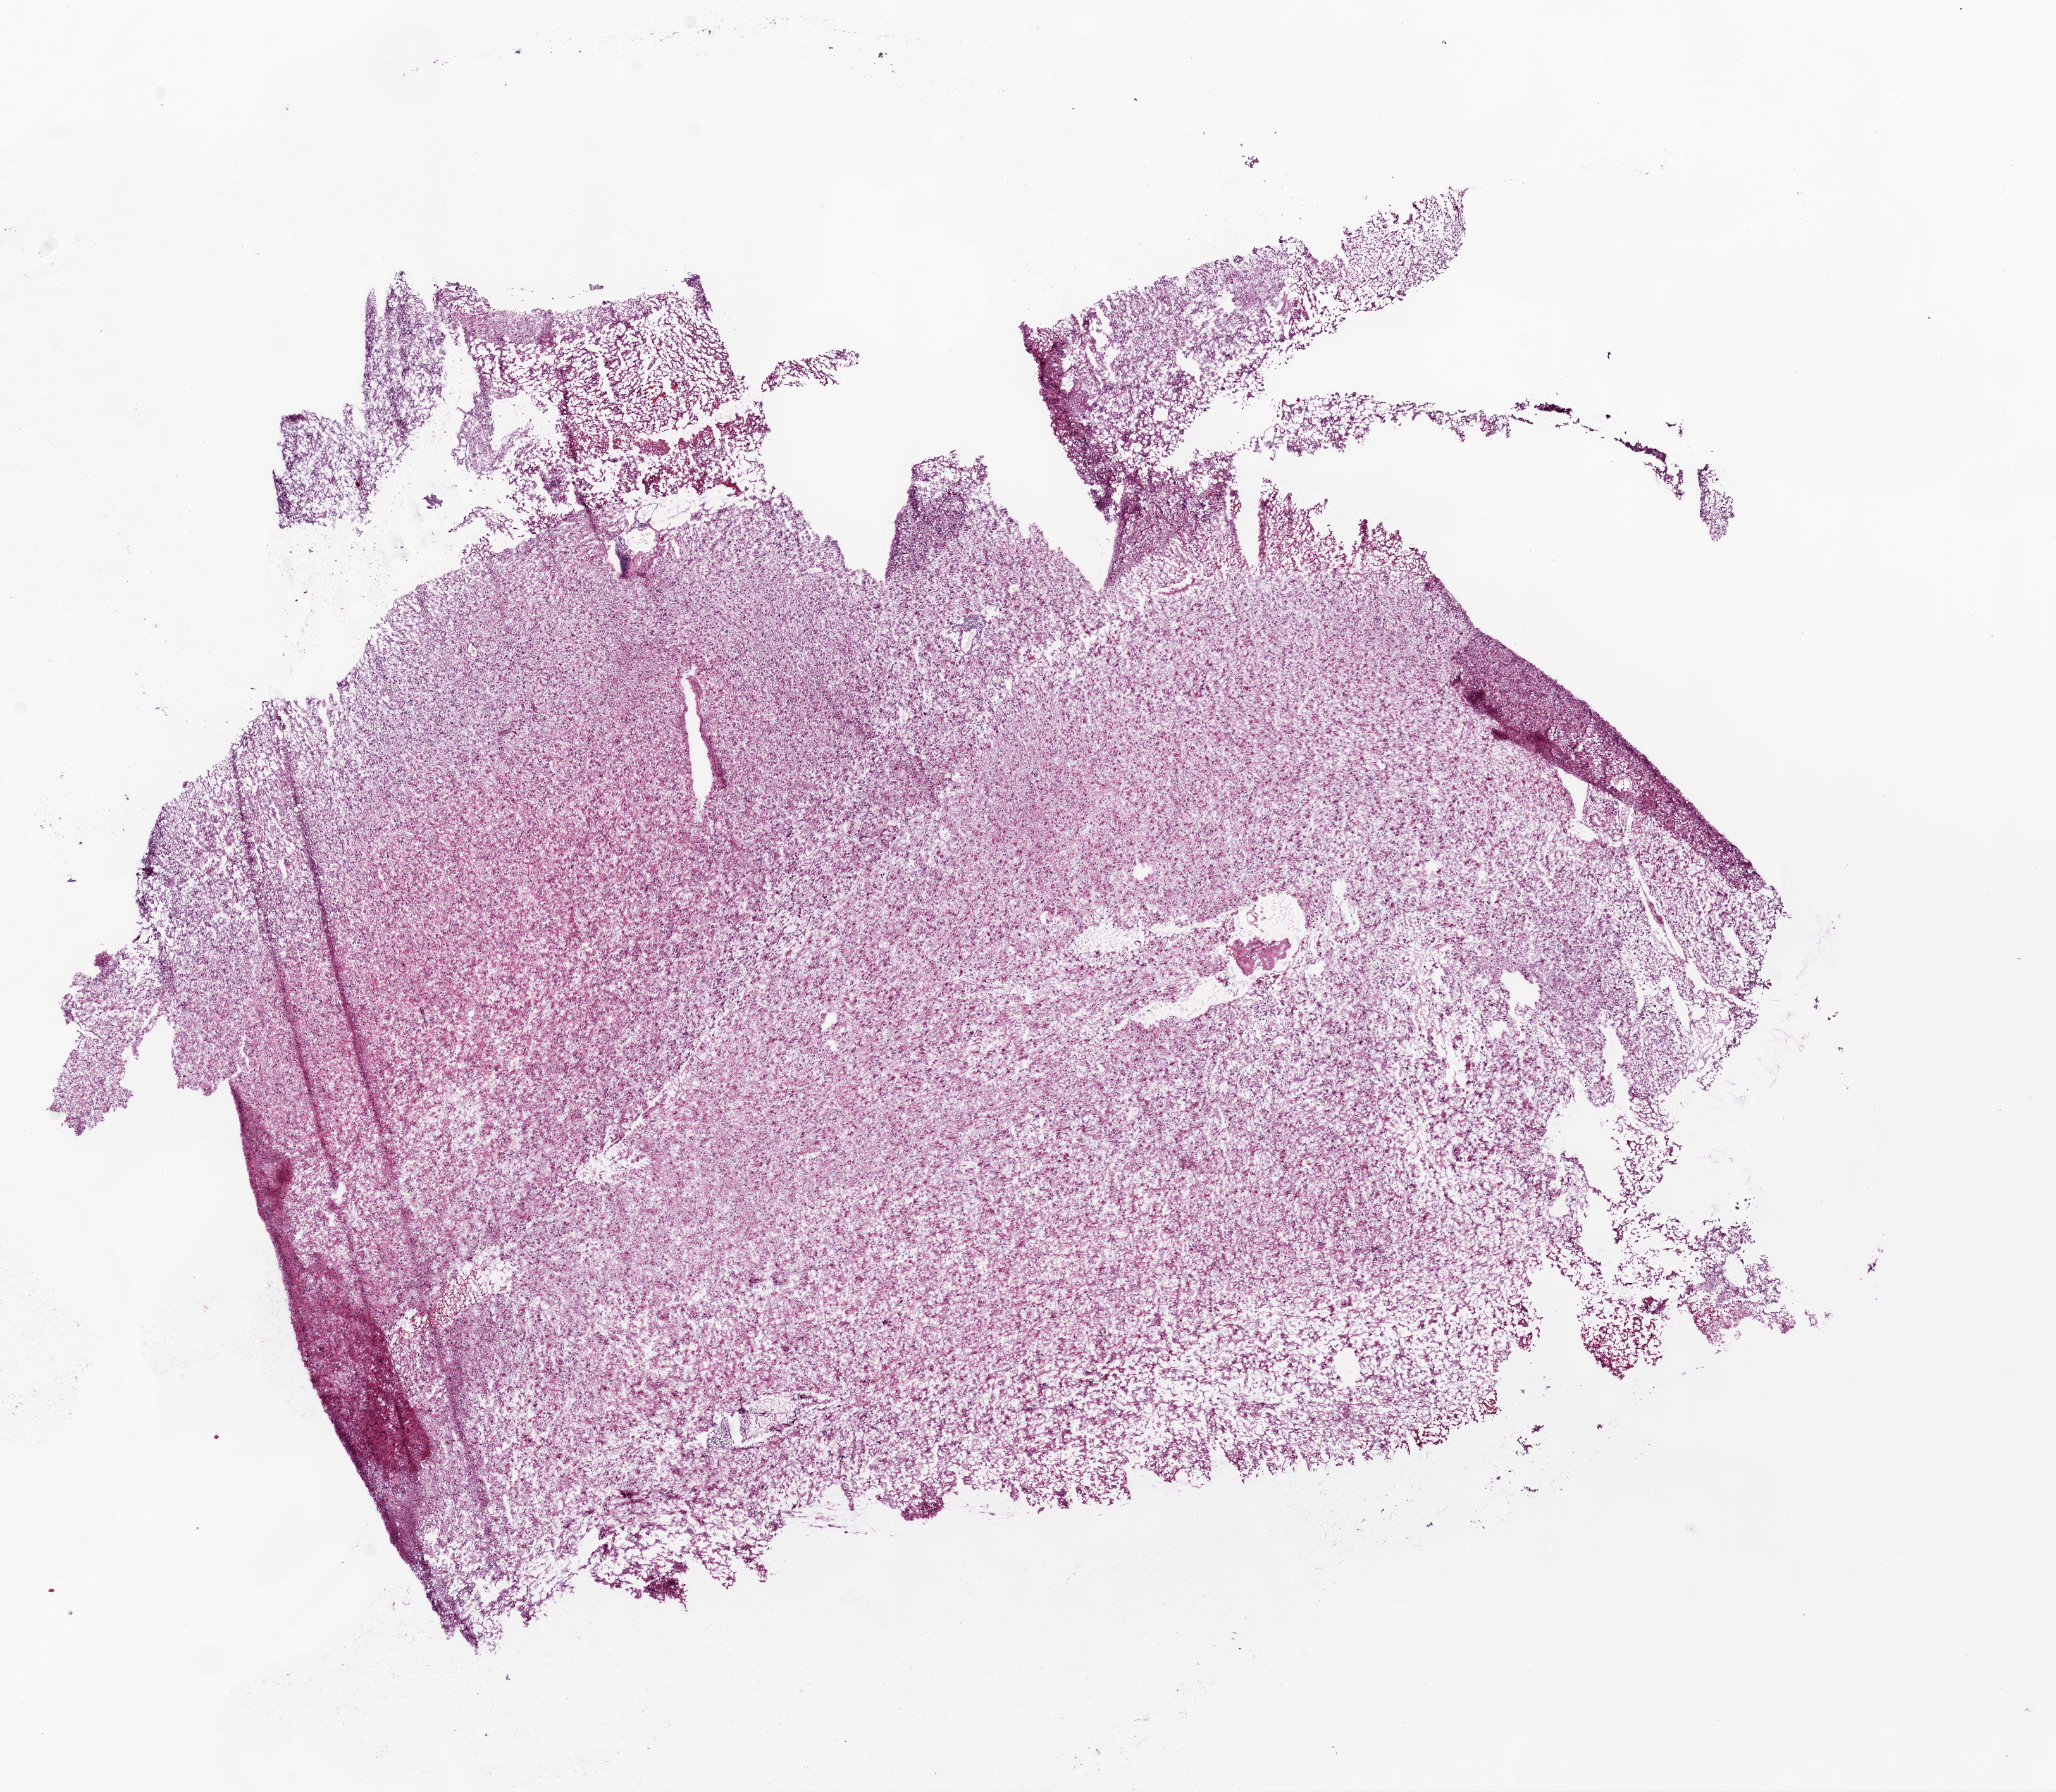
Digitized H&E tissue section (whole slide) — a low-resolution overview of the entire scanned area, about 13.0 x 11.4 mm; frozen section from the bottom of the tissue portion; brain, primary tumour sample. Patient: male, age at initial diagnosis 56 years. Slide review estimates, as recorded: tumour cells 80%, tumour nuclei 90%, normal cells 5%, stromal cells 15%, necrosis 0%. Infiltration values recorded for this section: lymphocyte infiltration 100%.
Pathologic diagnosis: Glioblastoma.